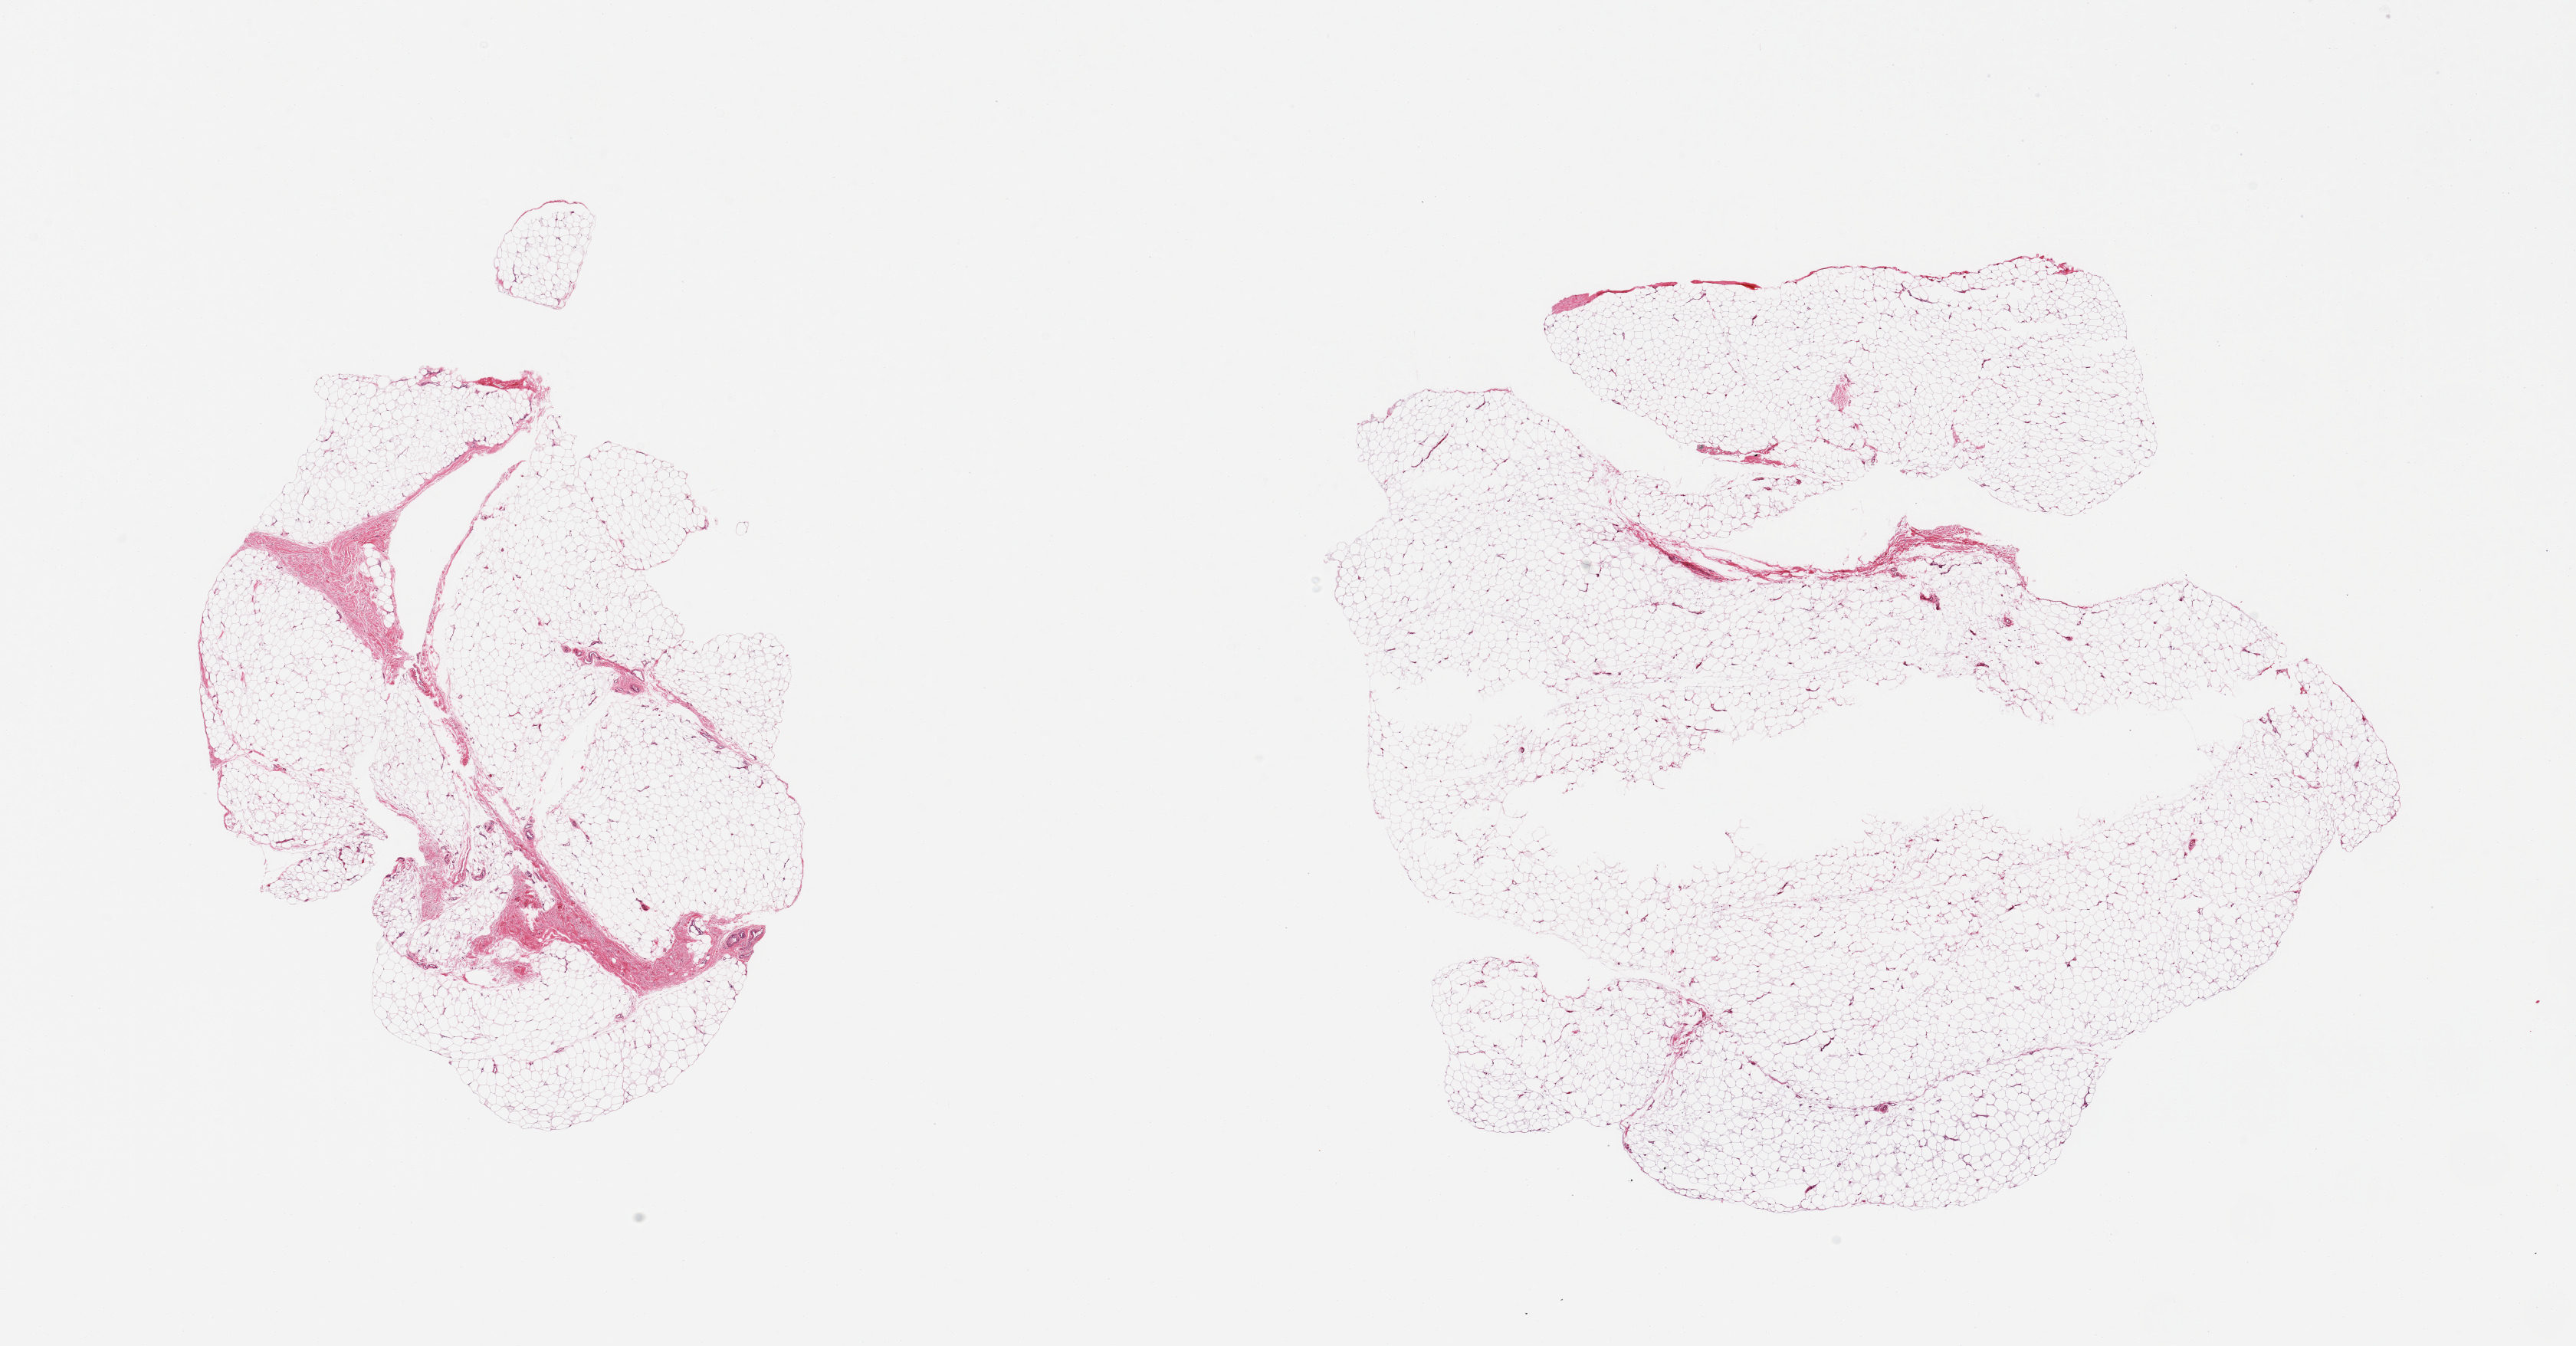
Whole-slide image, haematoxylin and eosin stain, low-resolution overview of the scanned area, about 26.6 x 13.9 mm (slide scanned at 20x), PAXgene-fixed, paraffin-embedded tissue, sampled site (target tissue): adipose tissue, donor tissue sample. Donor sex: male.
Review note (as recorded): 2 pieces; one has large central defect (?fixation).